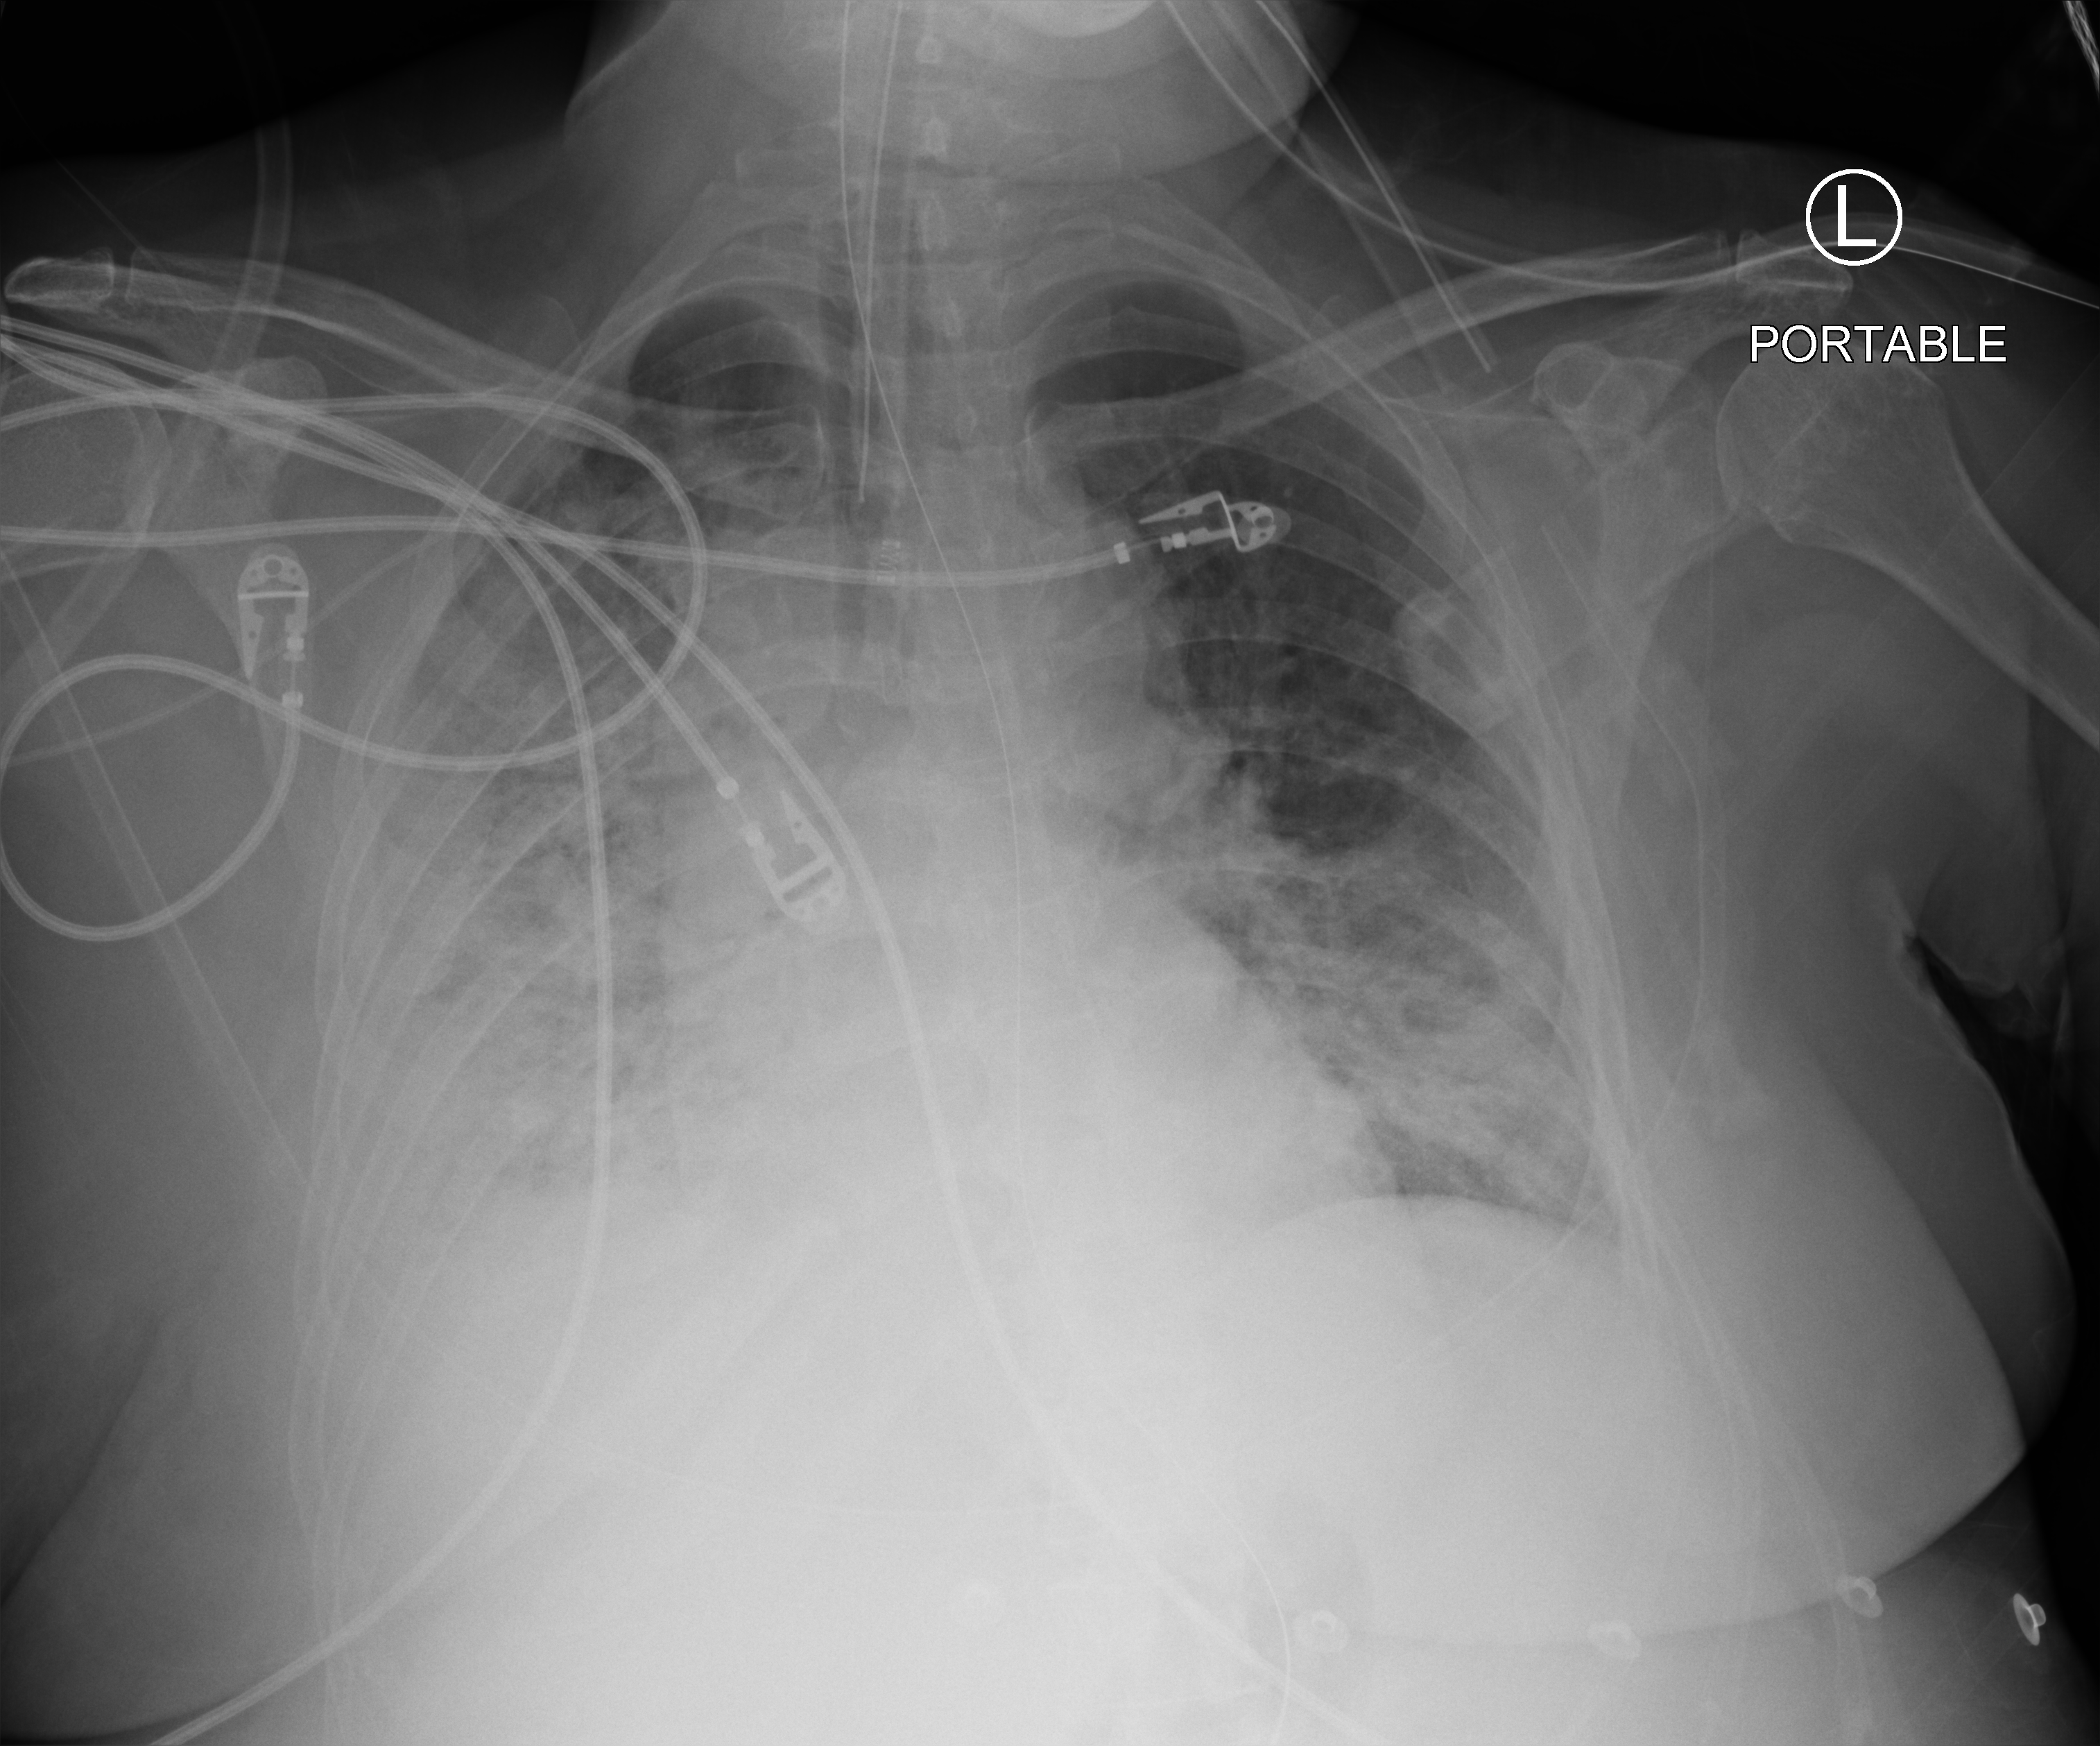
Chest X-ray (portable), anteroposterior (AP) projection. Female patient hospitalised with COVID-19, age 18–59 years.
Admission-level facts for this patient (not findings on this image; timing relative to this image not recorded):
- admitted to intensive care during this hospital stay: yes